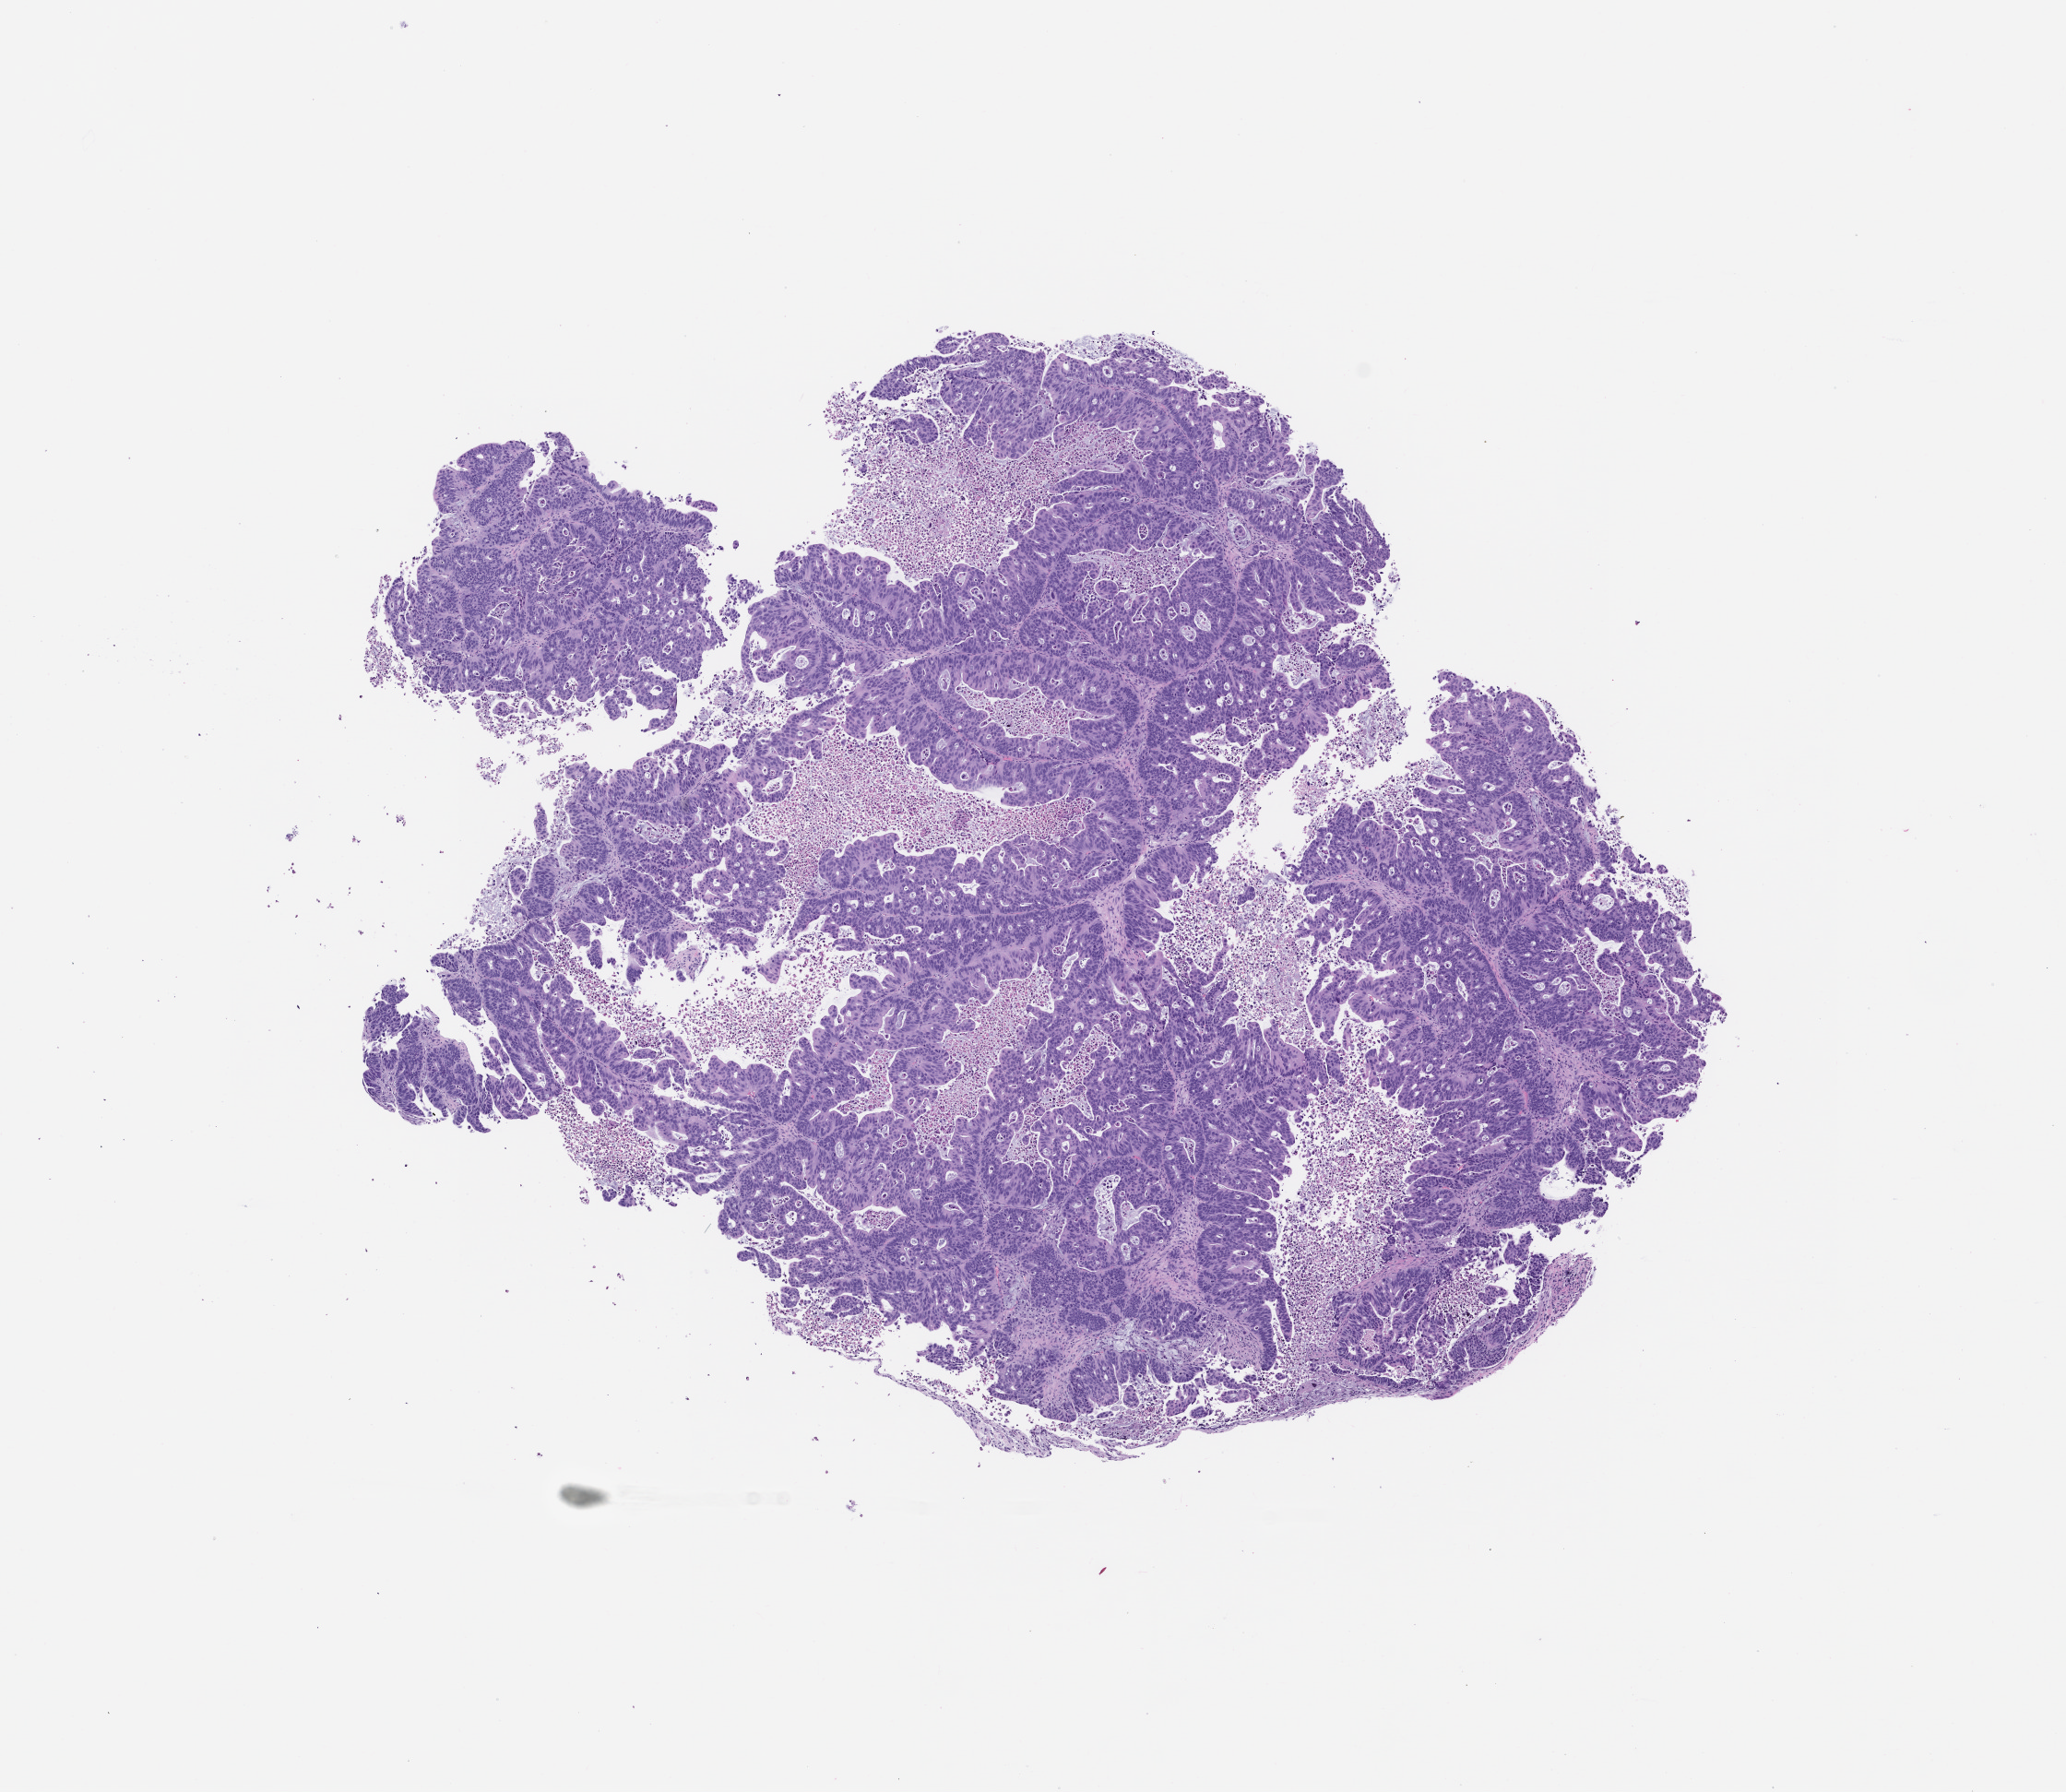
Hematoxylin and eosin (H&E) whole-slide image of a patient-derived xenograft (PDX) tumor grown in a mouse, passage 2 — a low-resolution overview of the entire scanned area, about 9.0 x 7.8 mm, formalin-fixed, paraffin-embedded (FFPE) tissue, tumor site category: colon.
Originating patient diagnosis: Colon Adenocarcinoma.